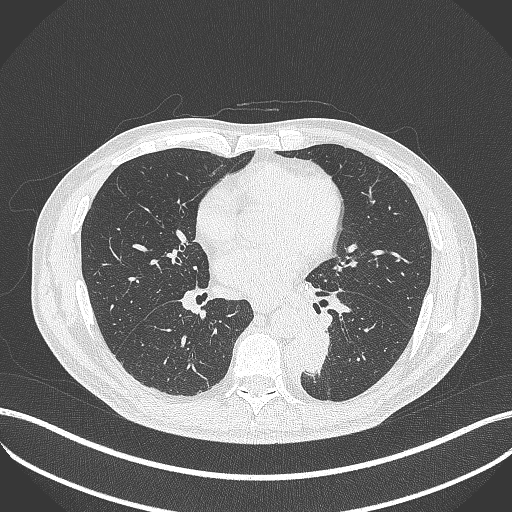
Chest CT, one axial slice. Slice 193 of 451 in the series (ordered by position). 120 kVp. Lung window (W 1500 / L -600 HU). 1 mm slice thickness. 512 × 512 image matrix, field of view 400 × 400 mm. Patient: male, 72 years. Case-level facts recorded for this patient, not image findings: clinical TNM (as recorded): T2b N0 M1.
Annotated regions visible in this slice (rectangle marked by the reading radiologist):
- lung tumour (recorded histology: adenocarcinoma): box from (x=303, y=325) to (x=335, y=381) px